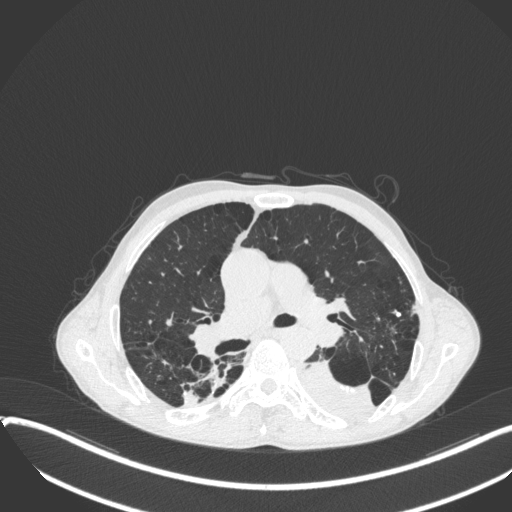
Chest CT, one axial slice. Position 231 of 400 along the scan axis. 120 kVp. Lung window (W 1500 / L -600 HU). 1 mm slice thickness. 512 × 512 image matrix, field of view 400 × 400 mm. Male patient, age 57 years. Case-level facts recorded for this patient, not image findings: clinical TNM (as recorded): T4 N0 M0.
Annotated regions visible in this slice (rectangle marked by the reading radiologist):
- lung tumour (recorded histology: squamous cell carcinoma): bounding box (x1, y1, x2, y2) in pixels: (294, 350, 383, 424)